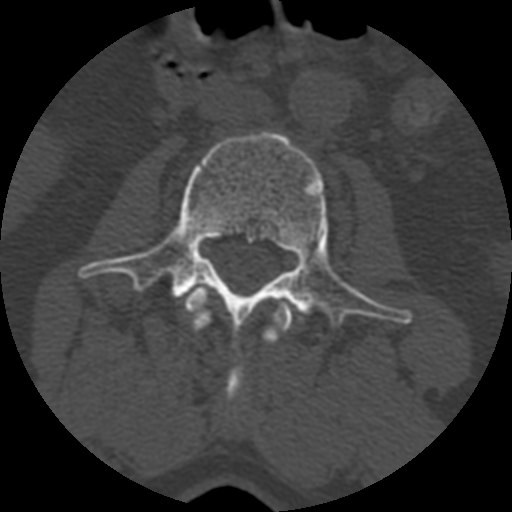
CT including the spine, one axial slice. Reconstruction kernel STANDARD. 120 kVp. Bone window (W 1800 / L 400 HU). 1.25 mm slice thickness. 512 × 512 image matrix, field of view 160 × 160 mm. Patient age 71 years. From the clinical record (not read from this slice): primary cancer: prostate.
Structures marked on this image (semi-automatically segmented with operator editing):
- L2 vertebra: box from (x=184, y=288) to (x=292, y=403) px
- L3 vertebra: (x=79, y=131)–(x=406, y=349)